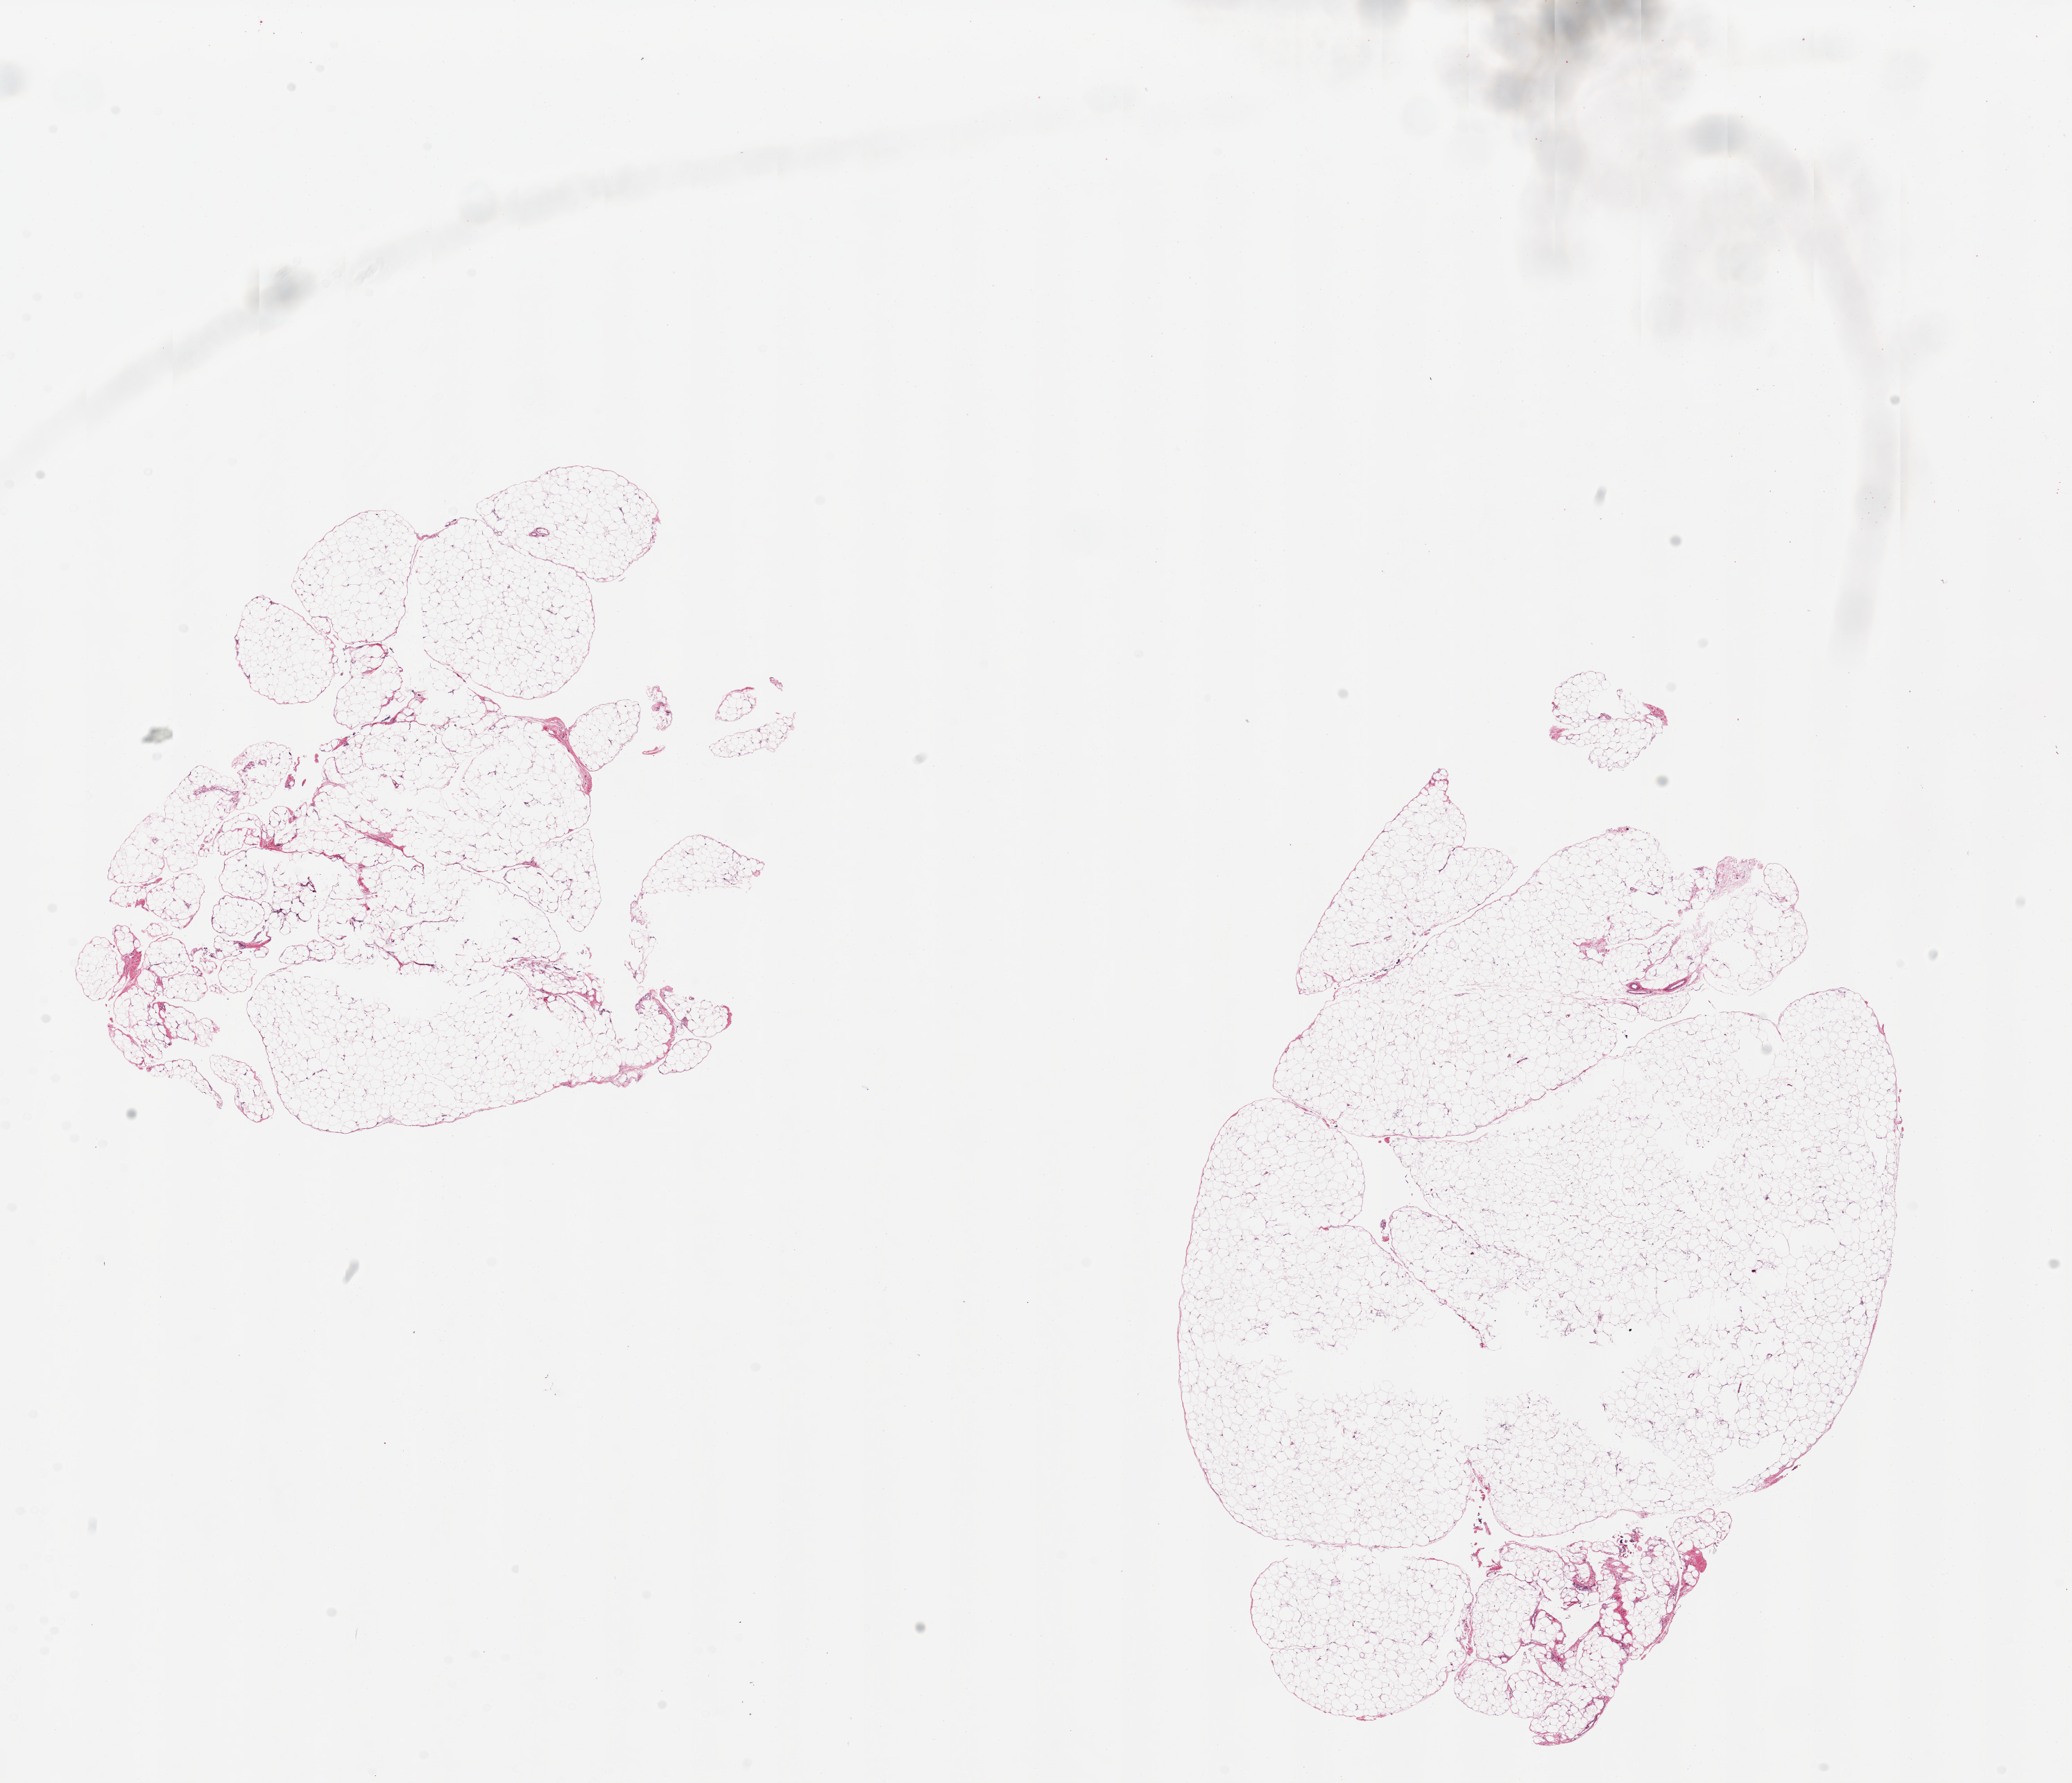
Hematoxylin and eosin (H&E) whole-slide image, brightfield, whole scanned area (about 23.6 x 20.3 mm) shown as a low-resolution overview. PAXgene-fixed, paraffin-embedded tissue. Section of omentum (target tissue). Tissue donor sample. Male donor.
* review note (as recorded): 2 pieces ~8x7mm